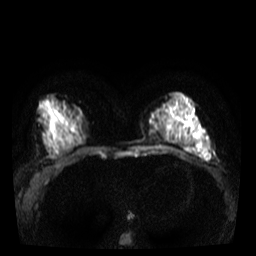
Breast MRI, one axial slice. Position 16 of 40 along the scan axis. Diffusion-weighted series; image 2 of 4 stored at this slice position (different b-values; order by instance number). 3 T. 5 mm slice thickness. 256 × 256 image matrix, field of view 320 × 320 mm. Female patient.
Annotated regions visible in this slice (outlined manually by an expert reader):
- tumour on diffusion-weighted imaging: bounding box [x1, y1, x2, y2] px = [203, 151, 210, 158]